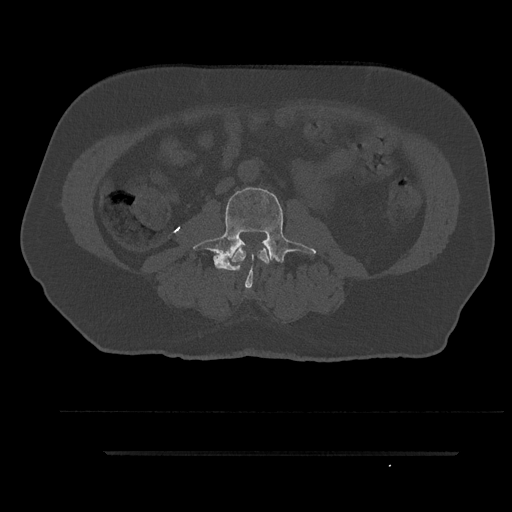
CT including the spine, one axial slice. Position 54 of 797 along the scan axis. 120 kVp. Bone window (W 1800 / L 400 HU). 512 × 512 image matrix, field of view 432 × 432 mm. Male patient, age 63 years. From the clinical record (not read from this slice): primary cancer: renal; vertebrae with lytic lesions (as recorded): T8.
Annotated regions visible in this slice (semi-automatically segmented with operator editing):
- L2 vertebra: box from (x=232, y=248) to (x=269, y=271) px
- L3 vertebra: (x=193, y=185)–(x=316, y=288)